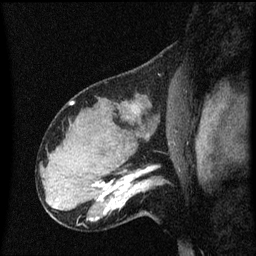
Breast MRI (dynamic contrast-enhanced), one sagittal slice; position 41 of 60 along the scan axis; dynamic contrast-enhanced series, image 2 of 3 at this slice position (ordered by acquisition); 1.5 T; TE 4.2 ms, TR 8.4 ms; 2 mm slice thickness; 256 × 256 image matrix. Patient: female, 31 years. From the clinical record (not read from this slice): setting: breast cancer imaged before/during neoadjuvant chemotherapy; receptor status: HR-positive, HER2-negative.
Annotated regions visible in this slice (semi-automatically segmented with operator editing):
- analysis volume of interest (the breast-tissue region the enhancement analysis was run in; not a lesion): bounding box <102,166,166,223> (left, top, right, bottom; pixels)
- tumour enhancement mask (voxels above the 70 % enhancement threshold inside the analysis volume of interest): <102,168,154,215>